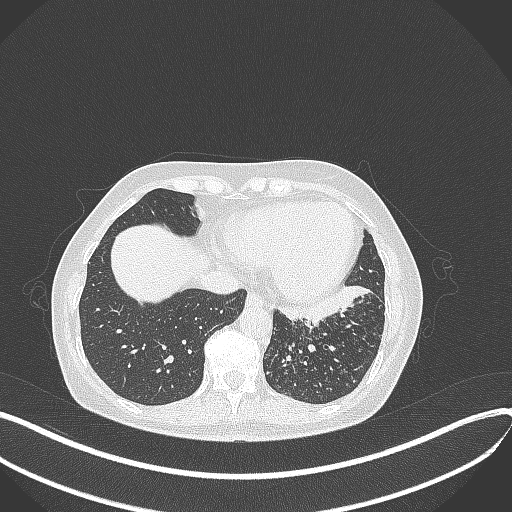
Chest CT, one axial slice. Position 112 of 429 along the scan axis. Reconstruction kernel B70f. 100 kVp. Lung window (W 1500 / L -600 HU). 1 mm slice thickness. 512 × 512 image matrix, field of view 400 × 400 mm. Patient: female, 63 years. From the clinical record (not read from this slice): clinical TNM (as recorded): T1b N0 M0; histopathological grade: G2-3.
Outlined on this slice (bounding box drawn by a radiologist):
- lung tumour (recorded histology: adenocarcinoma): bounding box [x1, y1, x2, y2] px = [278, 278, 374, 327]